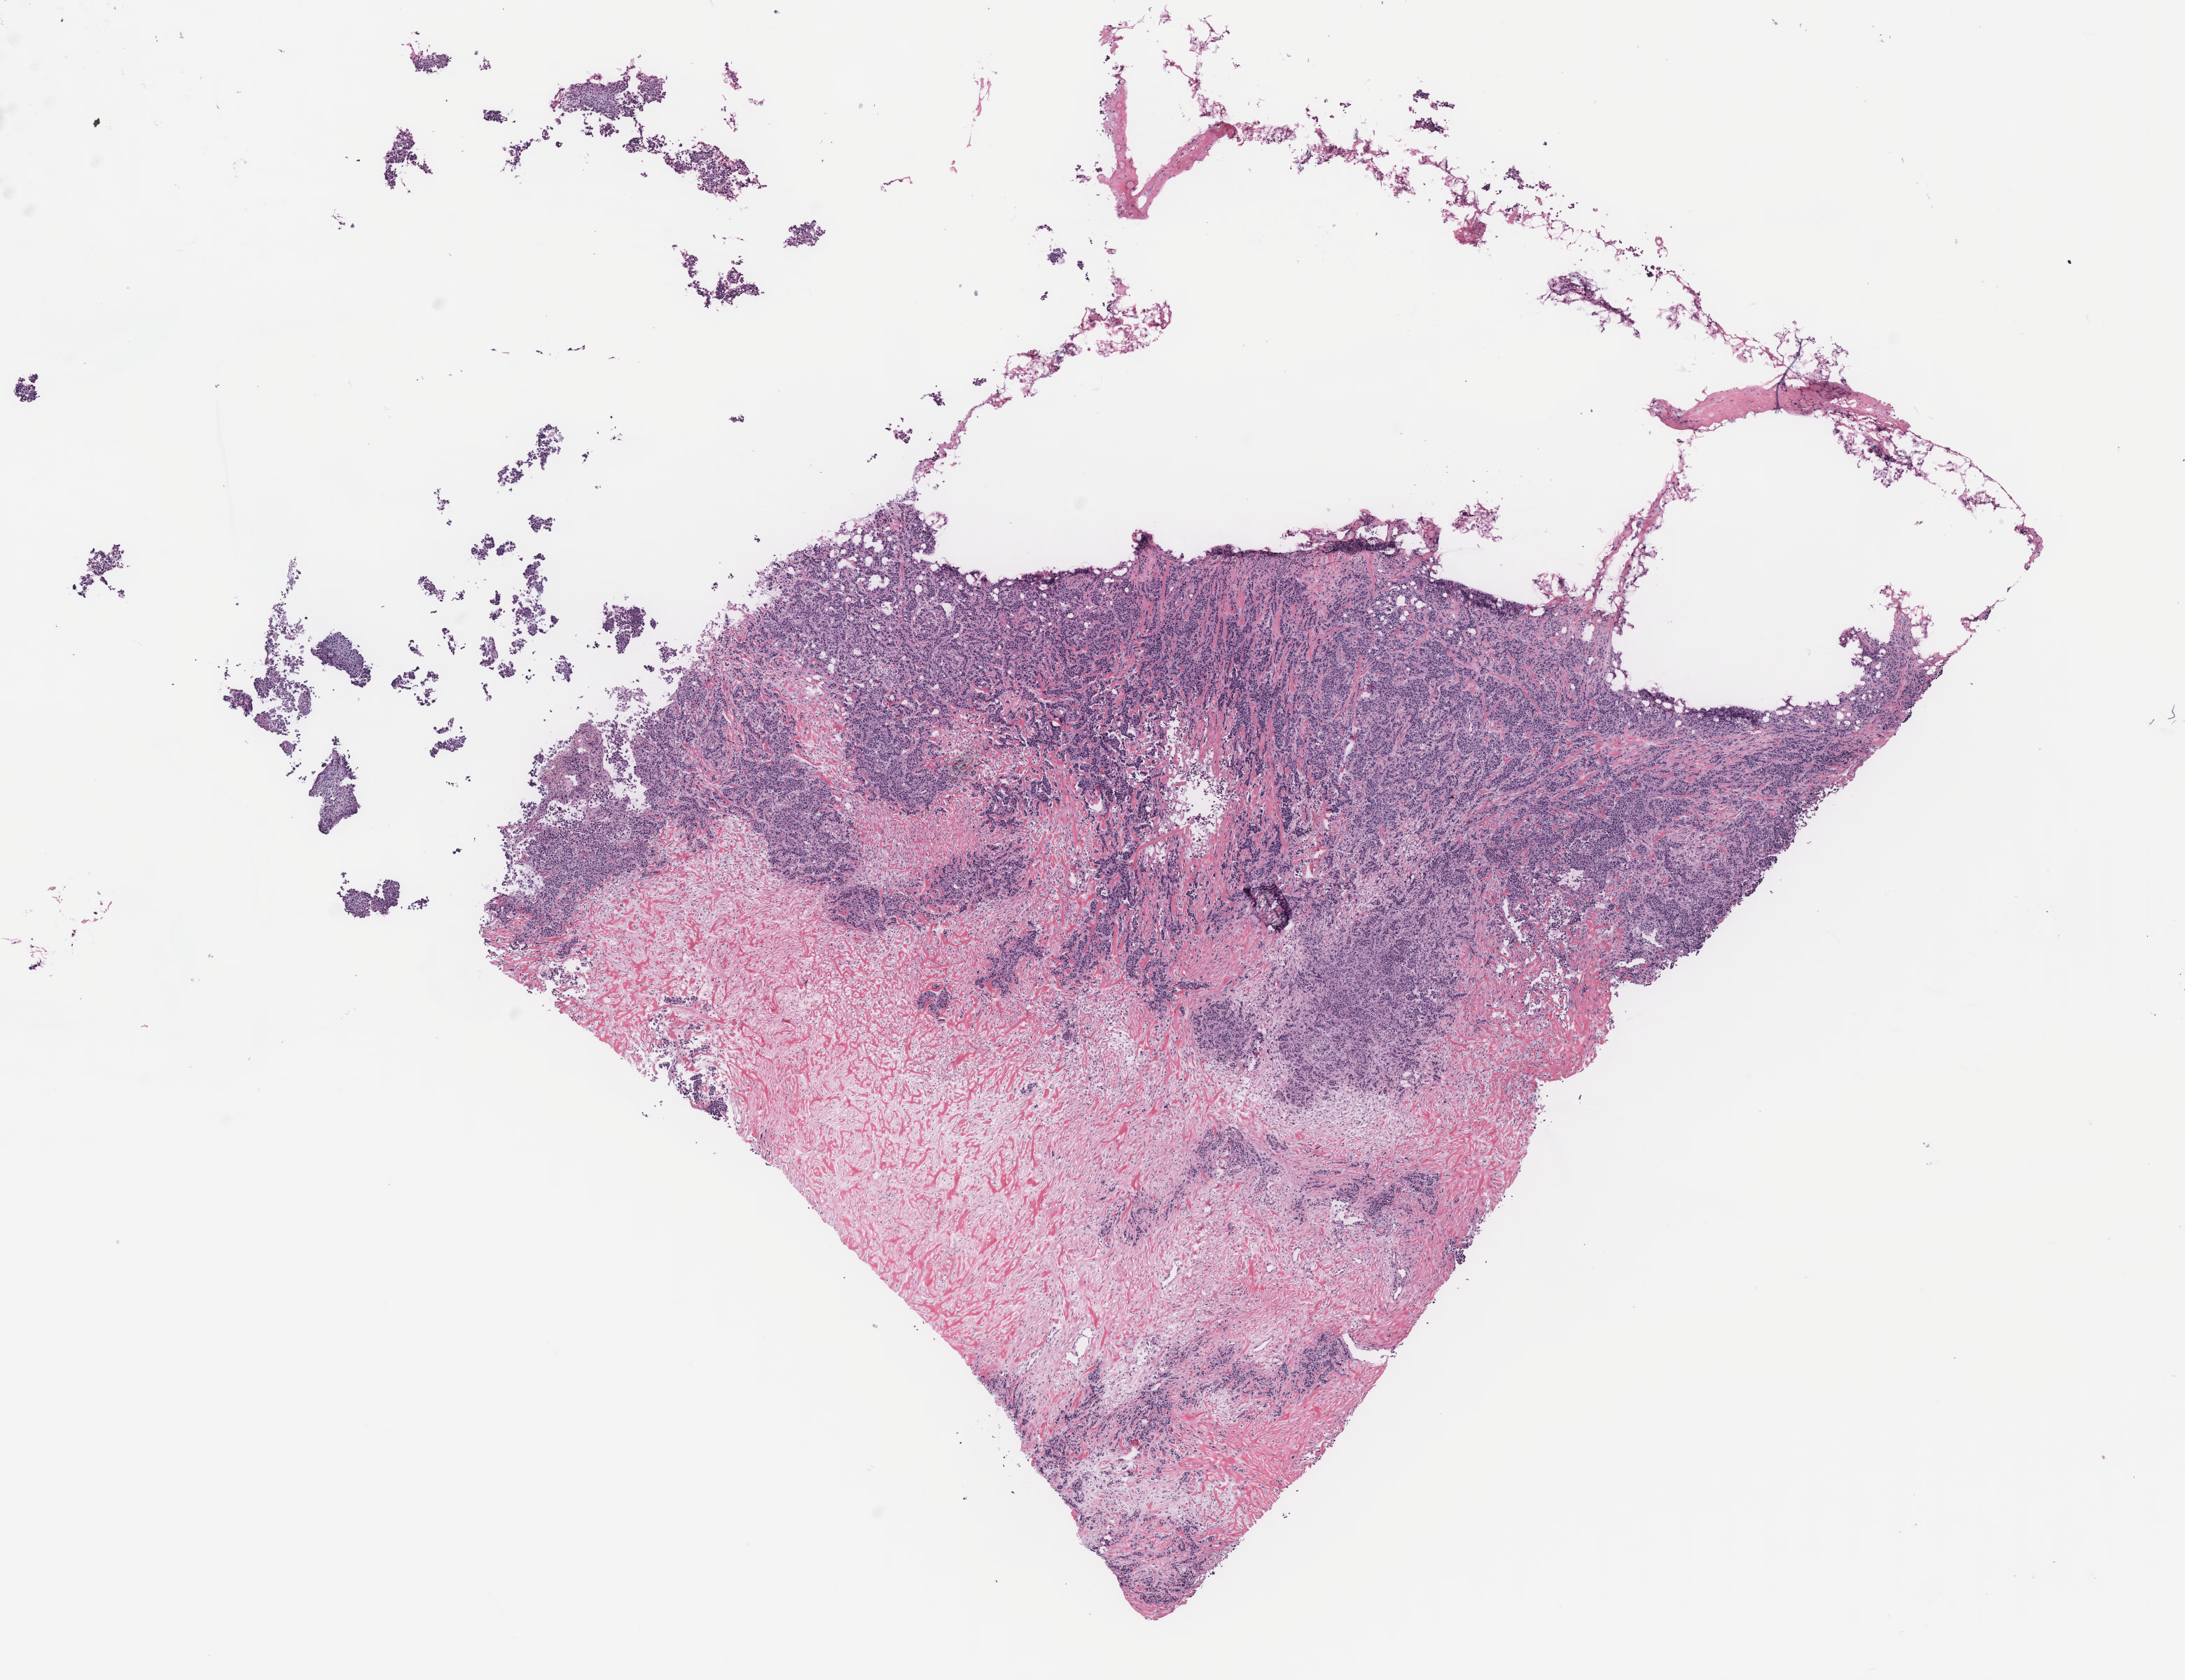
Whole-slide histology image, H&E — a low-resolution overview of the entire scanned area, about 12.5 x 9.6 mm; tumour tissue sample, breast. 75-year-old female patient.
• histologic diagnosis: Infiltrating duct carcinoma, NOS
• AJCC pathologic stage: IIIB